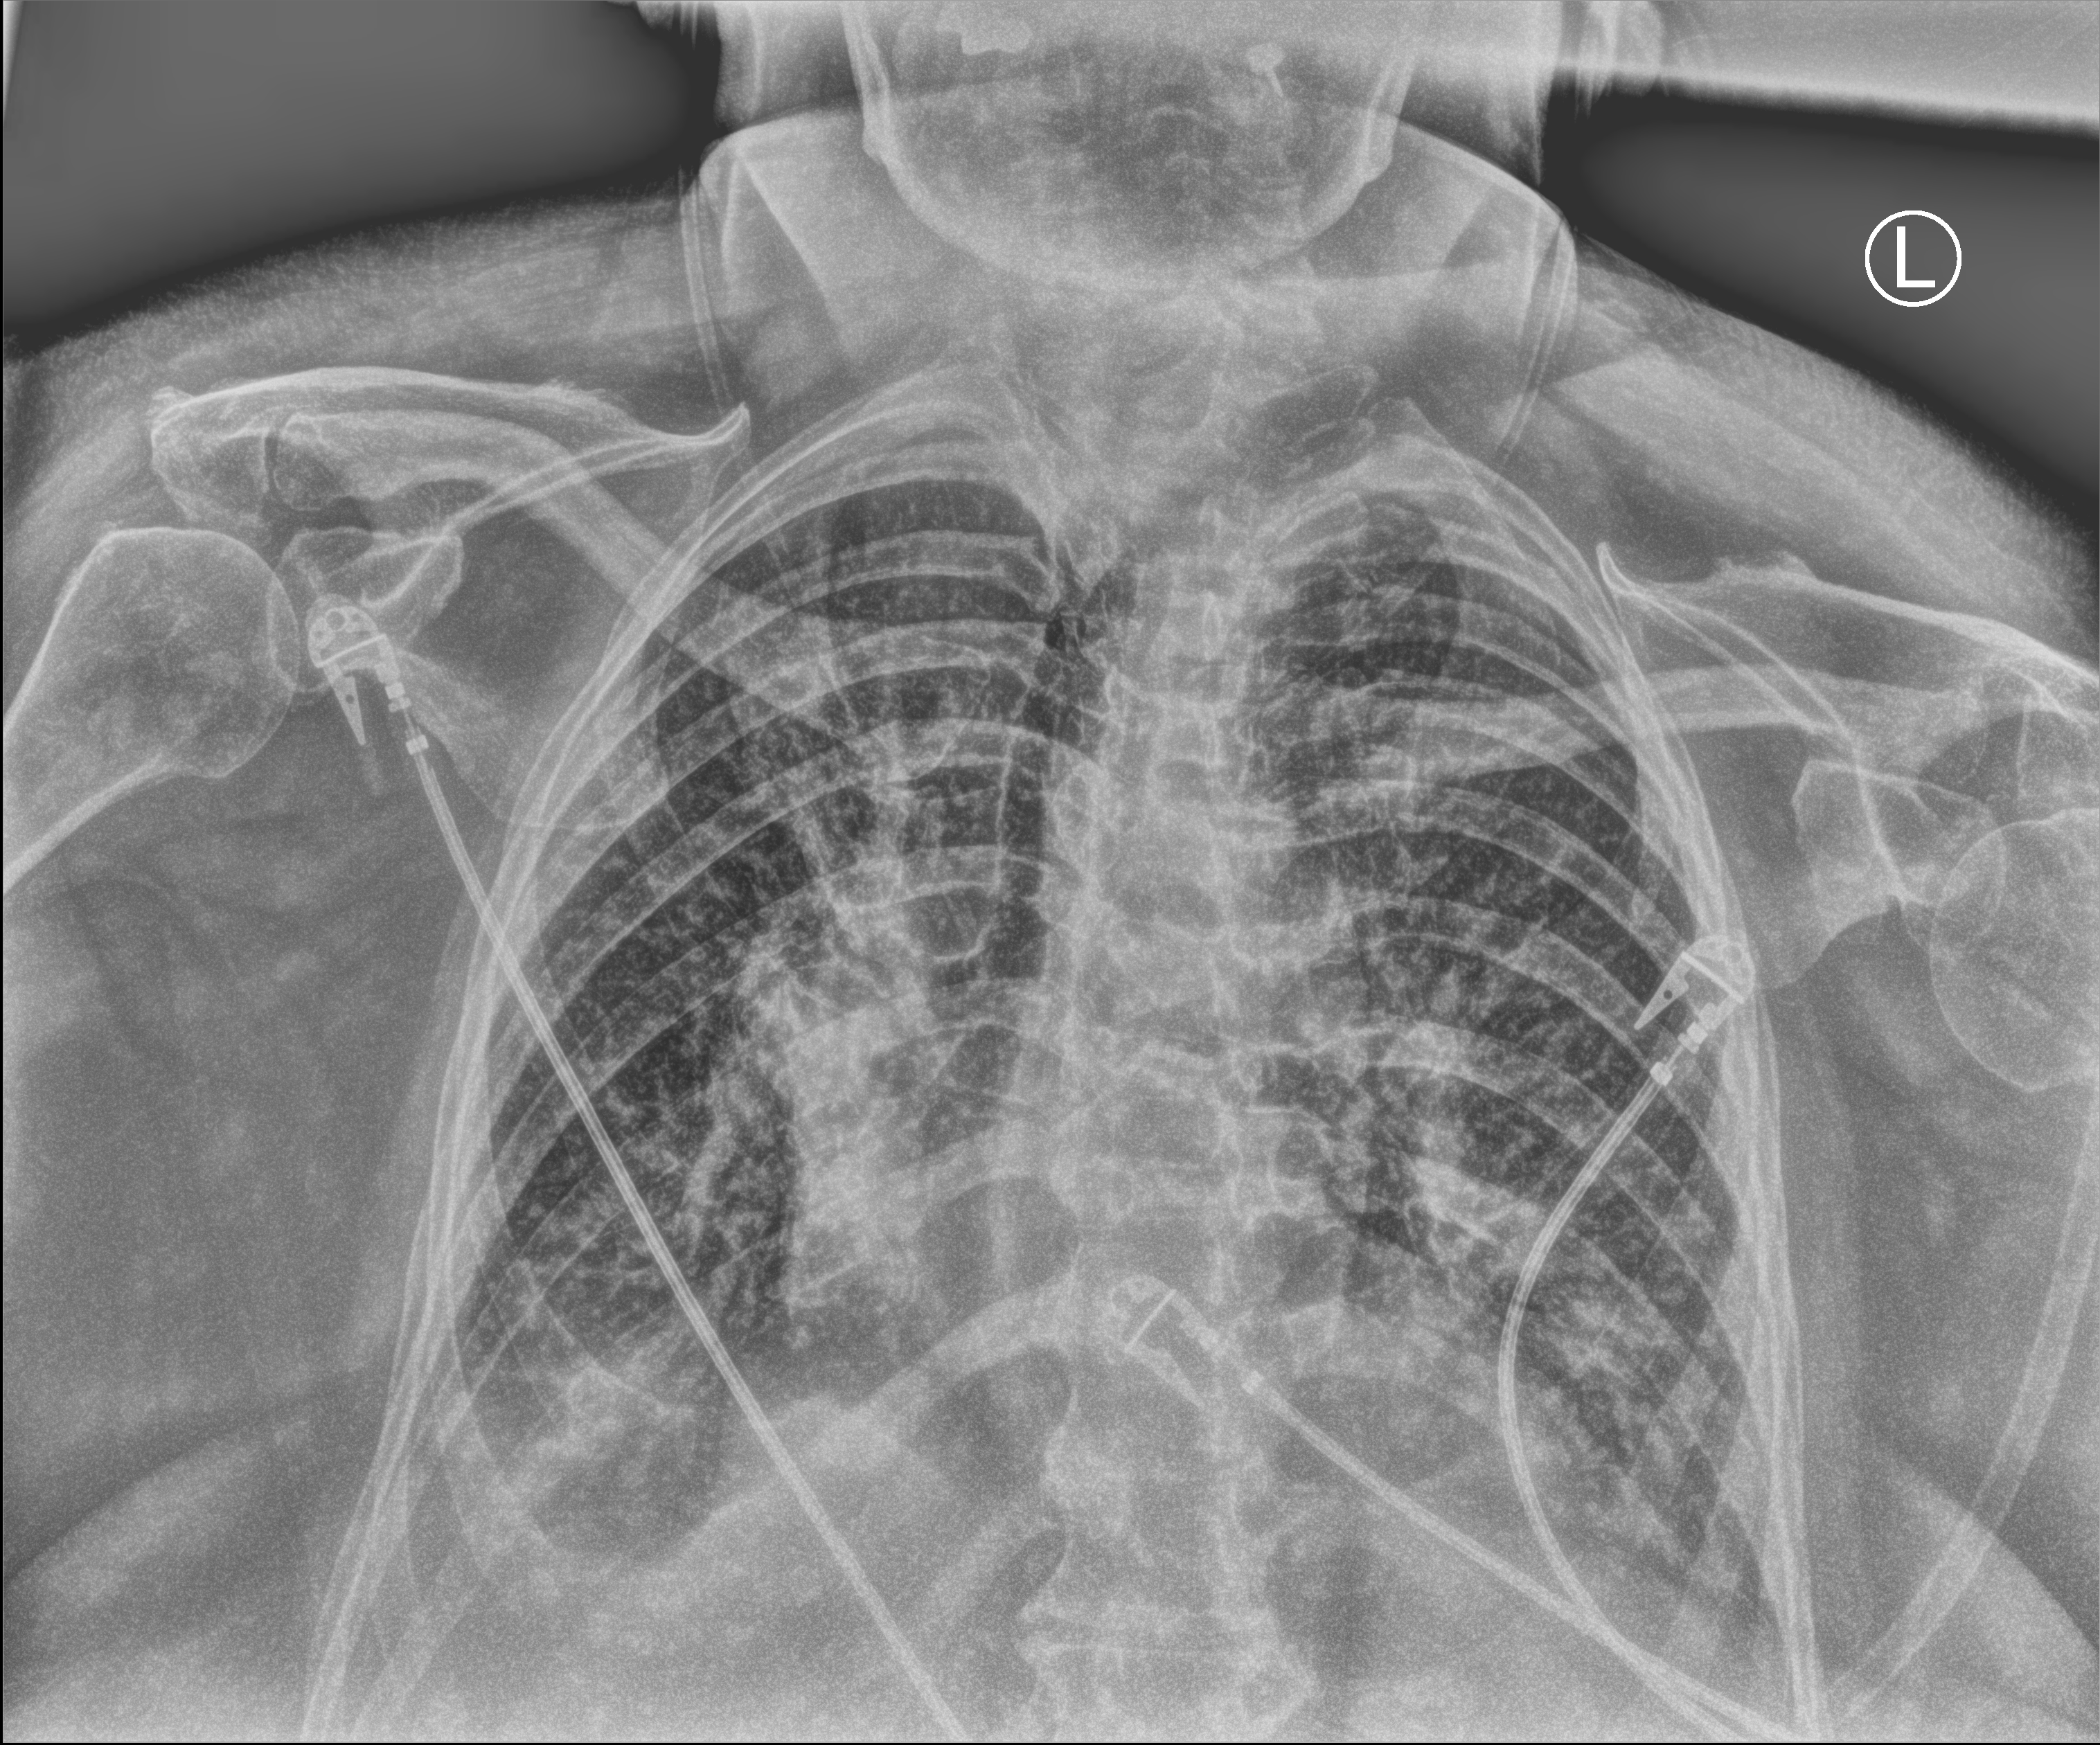
Portable chest radiograph; anteroposterior (AP) projection. Patient hospitalised with COVID-19; female, aged 75–90 years.
From the hospital-stay record, not from the radiograph (when in the stay this image was taken is not recorded):
- diabetes (admission record): no